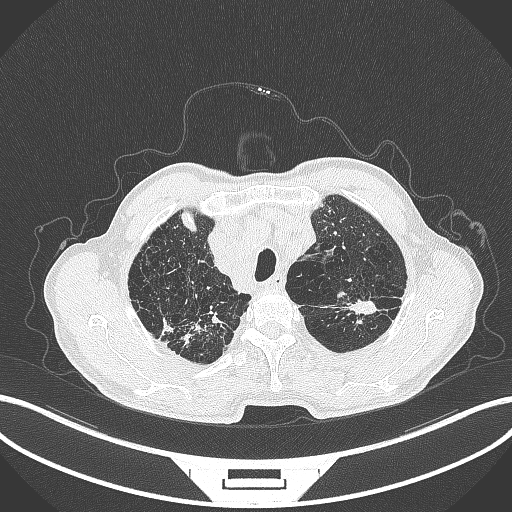
Chest CT, one axial slice. Slice 377 of 463 in the series (ordered by position). Reconstruction kernel B70f. 120 kVp. Lung window (W 1500 / L -600 HU). 1 mm slice thickness. 512 × 512 image matrix. Male patient, age 74 years. From the clinical record (not read from this slice): clinical TNM (as recorded): T2a N1 M0.
Outlined on this slice (bounding box drawn by a radiologist):
- lung tumour (recorded histology: adenocarcinoma): bounding box <333,293,377,317> (left, top, right, bottom; pixels)